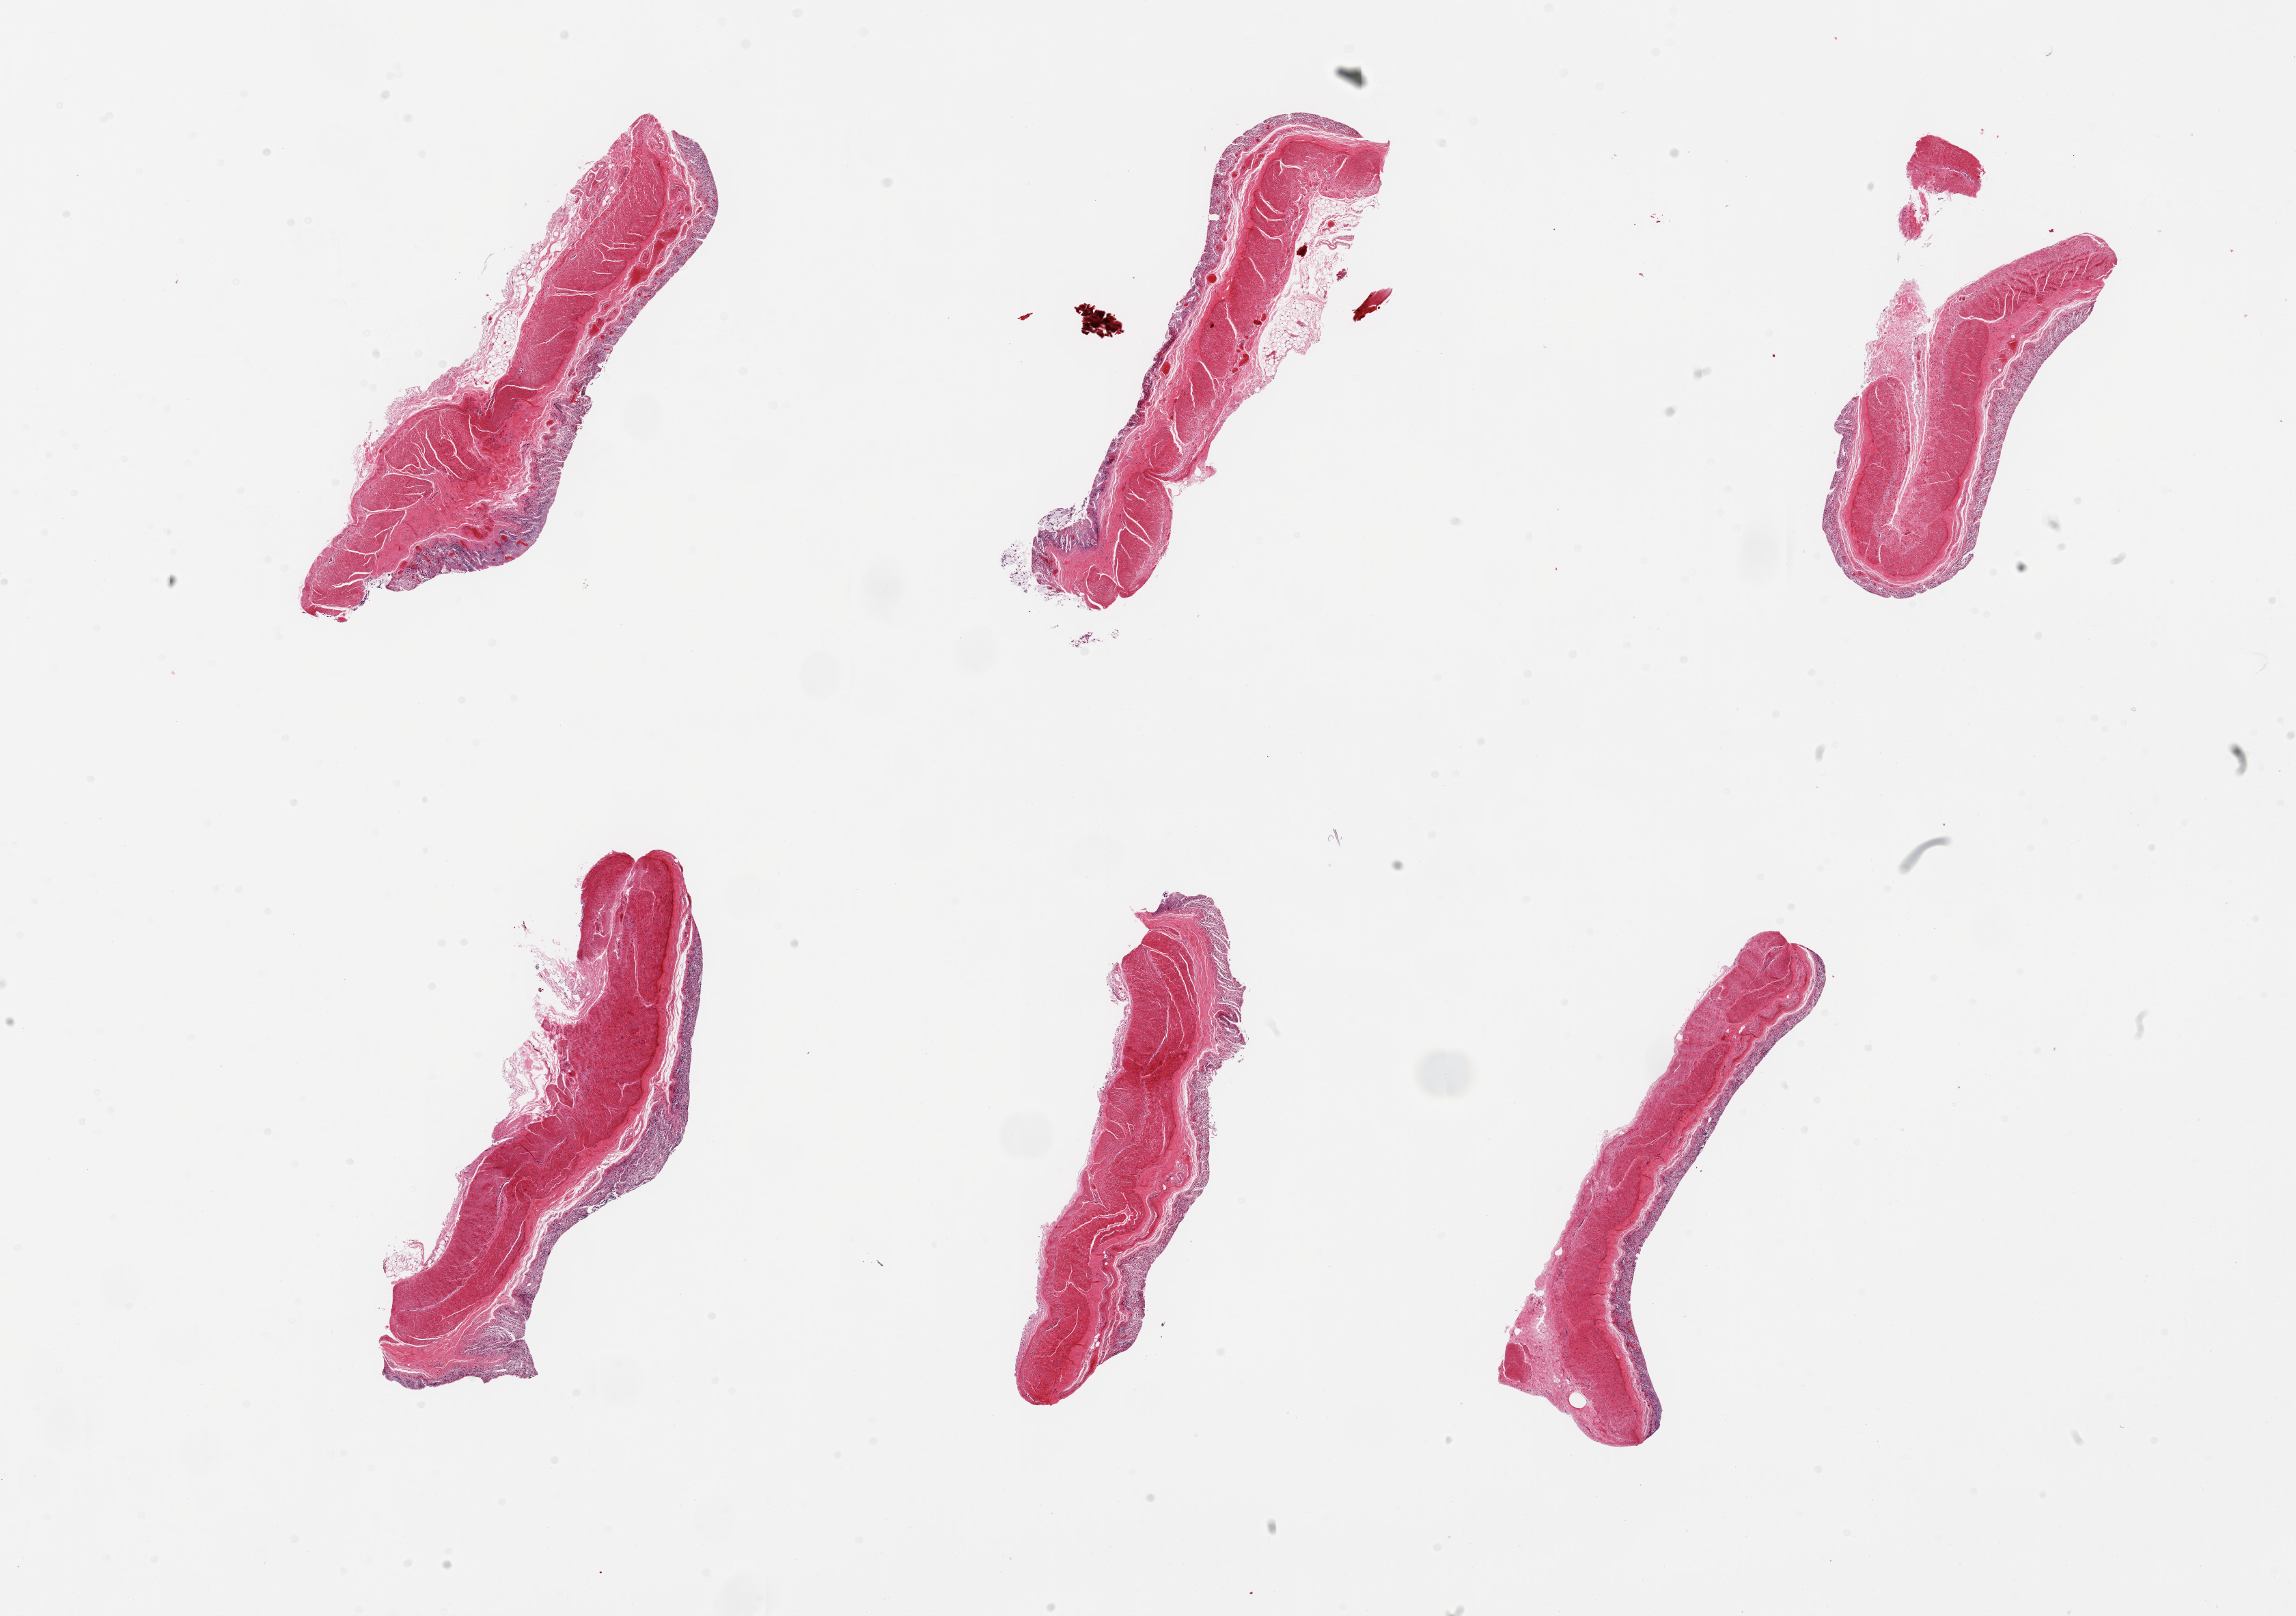
Digitized haematoxylin and eosin-stained section — low-resolution overview of the scanned area, about 26.6 x 18.7 mm (acquisition: 20x scan); PAXgene-fixed paraffin-embedded (PFPE) section; target tissue: transverse colon; tissue donor sample. Male donor.
• review note (as recorded): 6 pieces, mucosa partially sloughed, residual up to ~0.25mm, glandular elements completely autolyzed